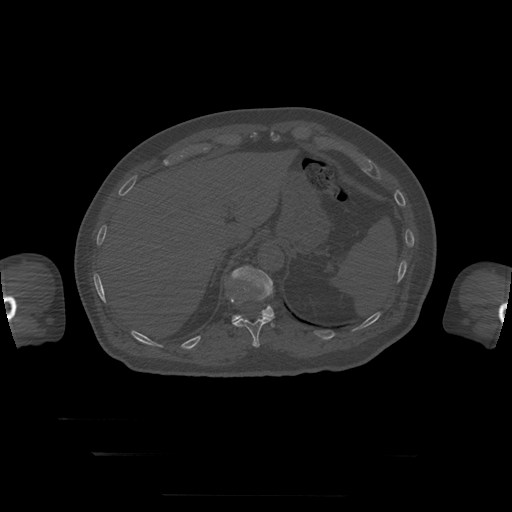
CT including the spine, one axial slice; slice 90 of 397 in the series (ordered by position); reconstruction kernel STANDARD; bone window (W 1800 / L 400 HU); 1.25 mm slice thickness; 512 × 512 image matrix, field of view 510 × 510 mm. Patient age 73 years. From the clinical record (not read from this slice): primary cancer: prostate.
Annotated regions visible in this slice (semi-automatically segmented with operator editing):
- T11 vertebra: bounding box [x1, y1, x2, y2] px = [233, 312, 275, 348]
- T12 vertebra: [231, 266, 275, 323]